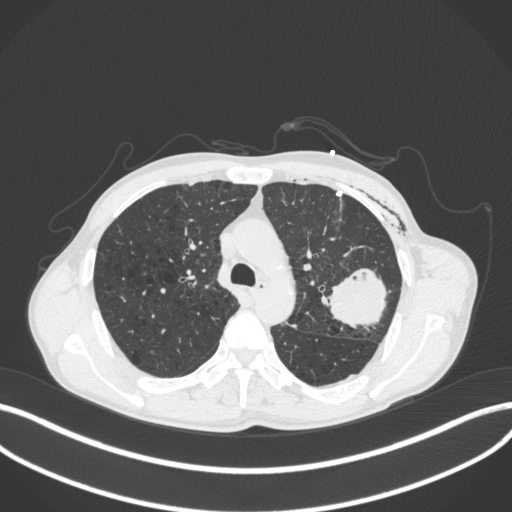
Chest CT, one axial slice; slice 280 of 416 in the series (ordered by position); reconstruction kernel B31f; 120 kVp; lung window (W 1500 / L -600 HU); 512 × 512 image matrix, field of view 400 × 400 mm. Patient: male, 58 years. From the clinical record (not read from this slice): clinical TNM (as recorded): T3 N0 M0.
Outlined on this slice (bounding box drawn by a radiologist):
- lung tumour (recorded histology: adenocarcinoma): box from (x=318, y=260) to (x=394, y=334) px